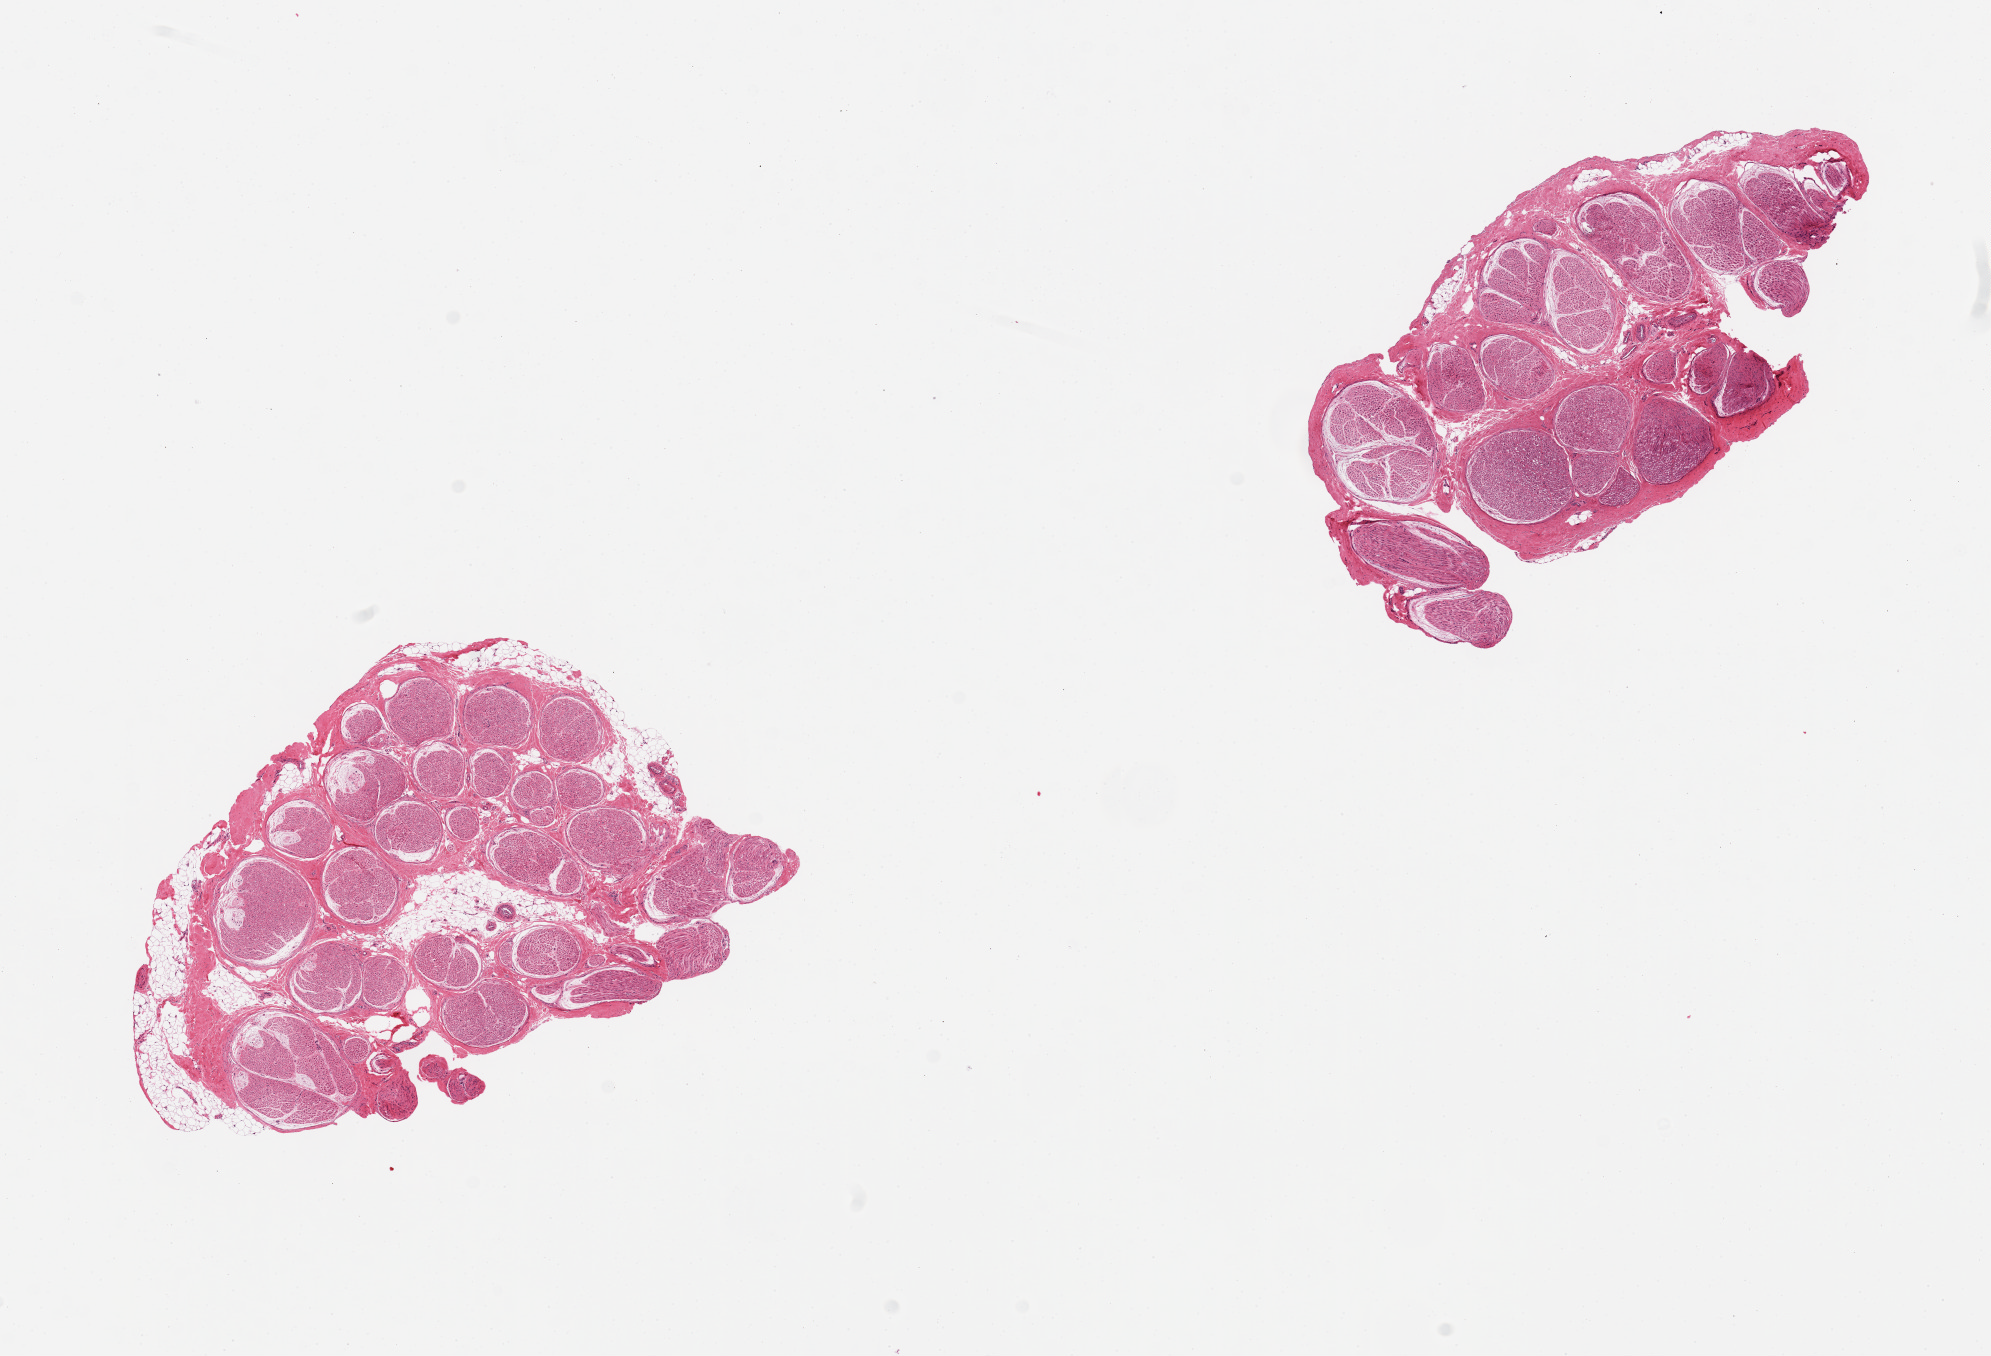
Whole-slide image, H&E stain, a low-resolution overview of the entire scanned area, about 15.8 x 10.7 mm, PAXgene-fixed, paraffin-embedded tissue, section of tibial nerve (target tissue), tissue donor sample. Donor sex: female.
Pathologist's review note for this sample: 2 pieces, clean specimens, minimal adherent fat.